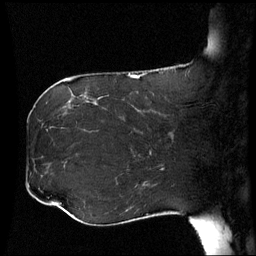
Breast MRI (dynamic contrast-enhanced), one sagittal slice. Position 23 of 60 along the scan axis. Dynamic contrast-enhanced series, image 2 of 3 at this slice position (ordered by acquisition). 1.5 T. TE 4.2 ms, TR 8.9 ms. 2.5 mm slice thickness. 256 × 256 image matrix. Female patient, age 42 years. Case-level facts recorded for this patient, not image findings: setting: breast cancer imaged before/during neoadjuvant chemotherapy; receptor status: HER2-positive.
Annotated regions visible in this slice (semi-automatic segmentation, software-assisted and operator-edited):
- analysis volume of interest (the breast-tissue region the enhancement analysis was run in; not a lesion): bounding box (x1, y1, x2, y2) in pixels: (106, 102, 173, 150)
- tumour enhancement mask (voxels above the 70 % enhancement threshold inside the analysis volume of interest): (154, 111, 160, 114)